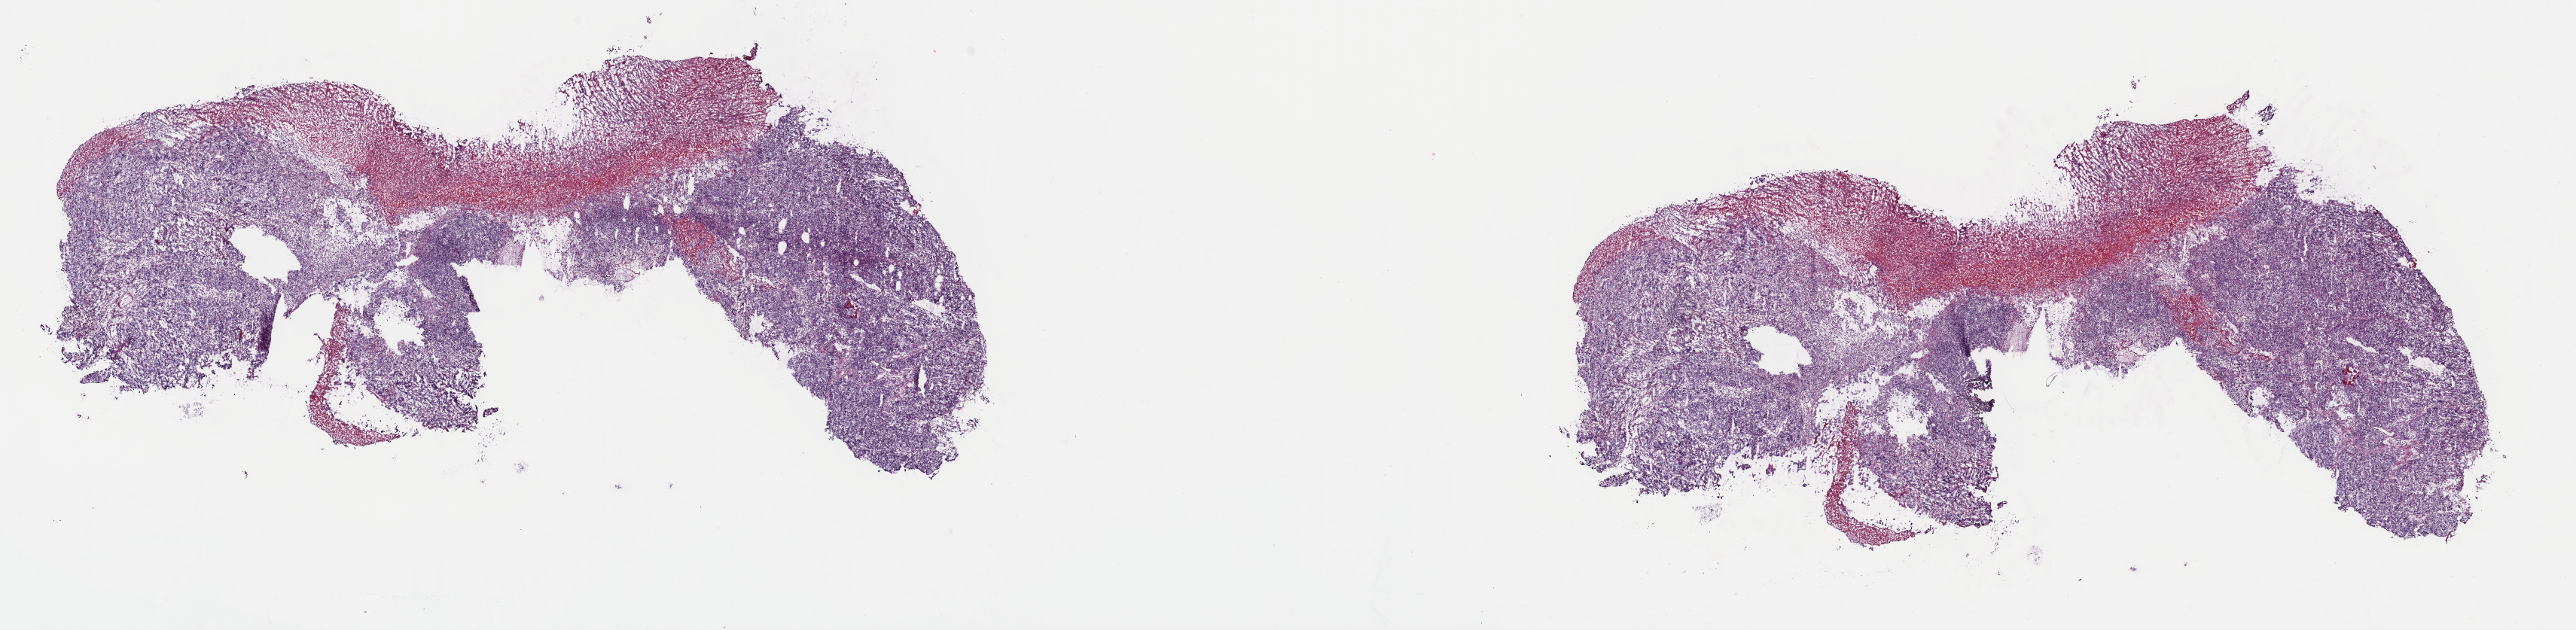
Whole-slide histology image, H&E-stained — shown as a low-resolution overview of the whole scanned area (about 27.0 x 6.6 mm), frozen section from the top of the tissue portion, primary tumour sample from the esophagus. Female patient. Histologic grade: G3 (poorly differentiated). Slide review estimates, as recorded: tumour cells 85%, tumour nuclei 92%, normal cells 0%, stromal cells 15%, necrosis 0%. Infiltration values recorded for this section: lymphocyte infiltration 0%, monocyte infiltration 0%, neutrophil infiltration 0%.
Pathologic diagnosis: Adenocarcinoma, NOS (lower third of esophagus). AJCC pathologic stage: IIB (7th edition). Lymph nodes positive (case pathology): 1 of 13 examined.